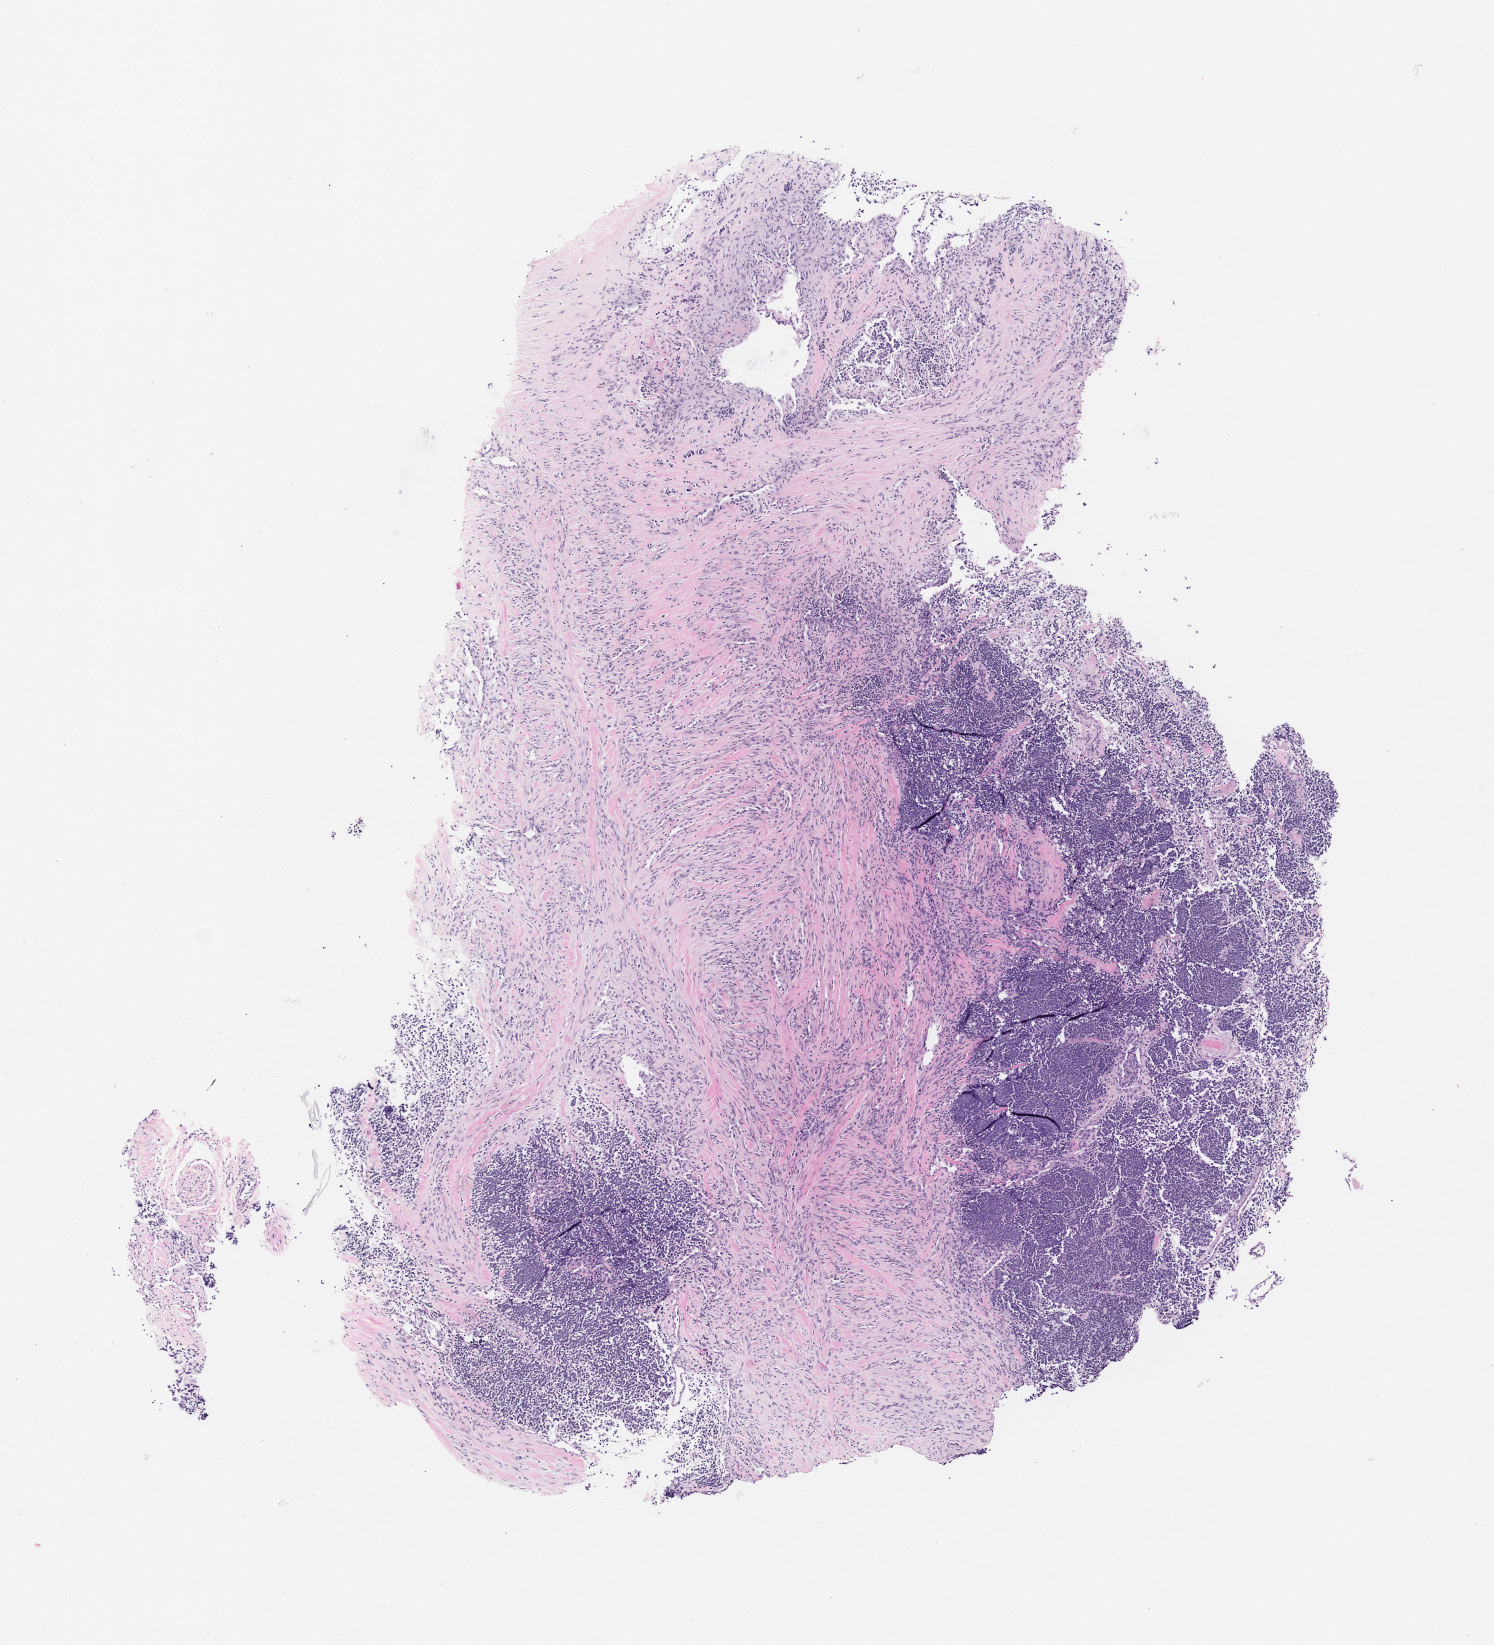
H&E whole-slide image of the patient's (originator) tumor tissue — shown as a low-resolution overview of the whole scanned area (about 6.0 x 6.6 mm). Formalin-fixed, paraffin-embedded (FFPE) tissue. Originating tumor site category: endocrine. Male patient, age 57 years.
Diagnosis: Merkel Cell Carcinoma.